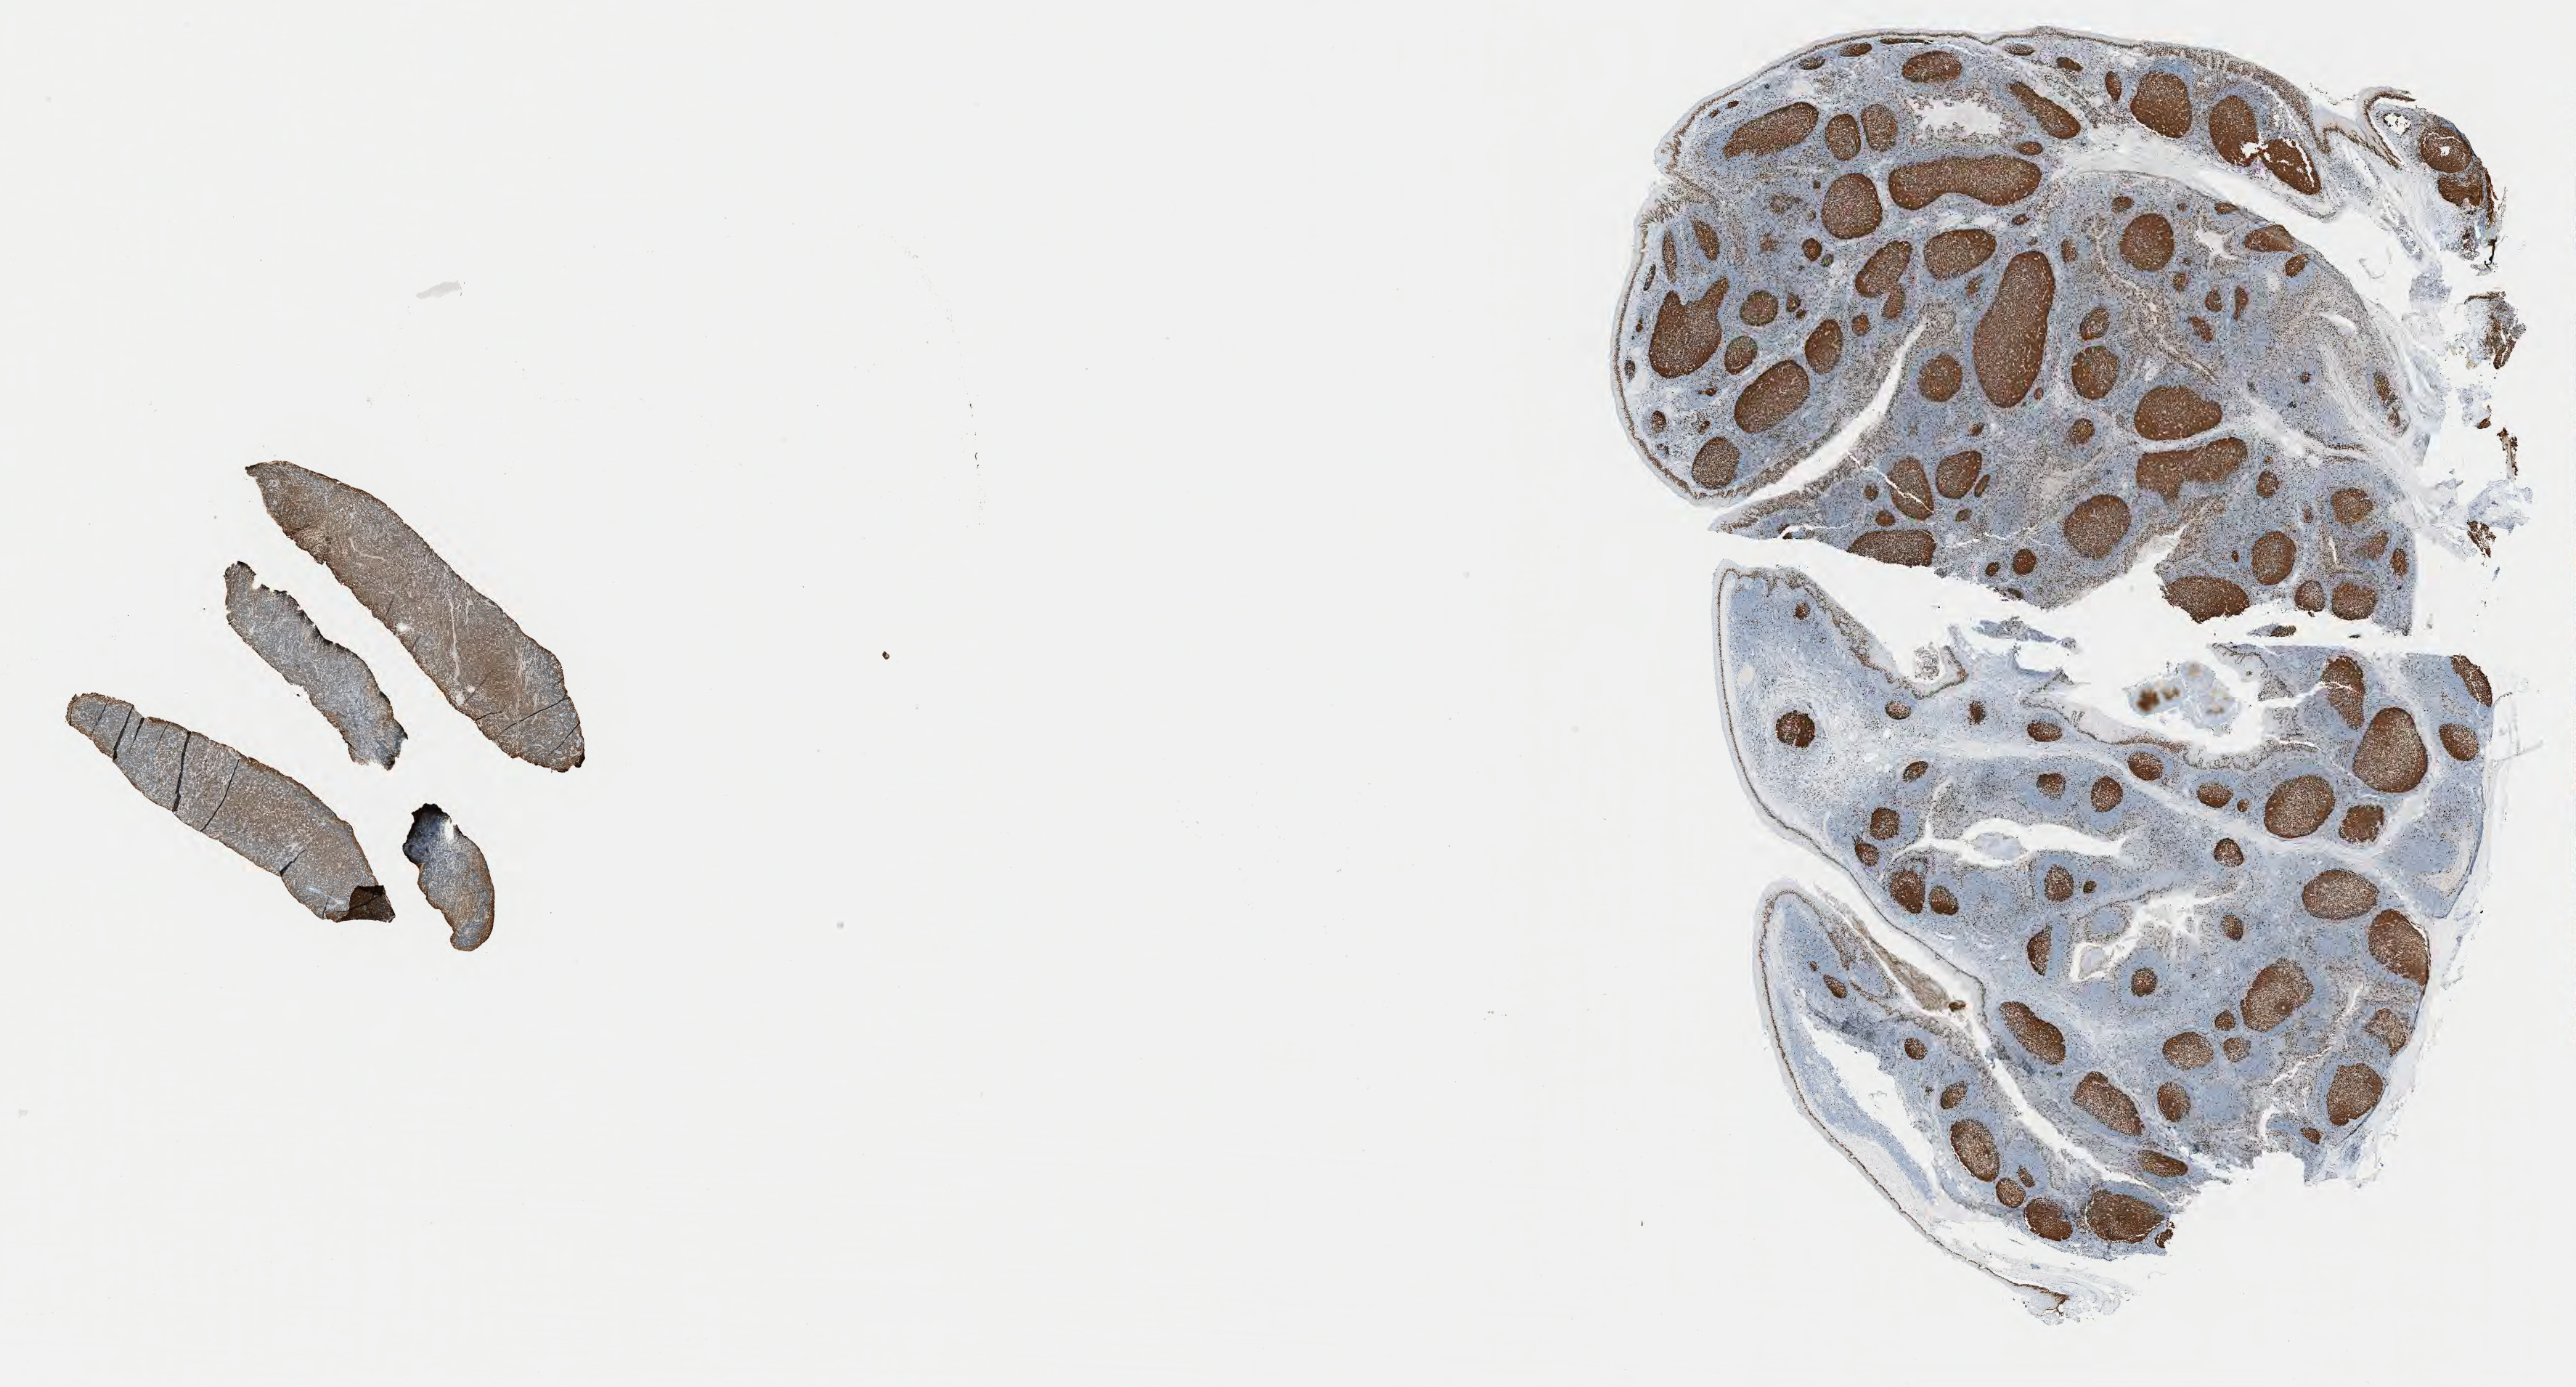
Whole-slide image, immunohistochemical stain for Ki-67 — a low-resolution overview of the entire scanned area, about 28.7 x 15.4 mm, tumor tissue. Female patient, 46 years old.
Diagnosis: Burkitt lymphoma, NOS.